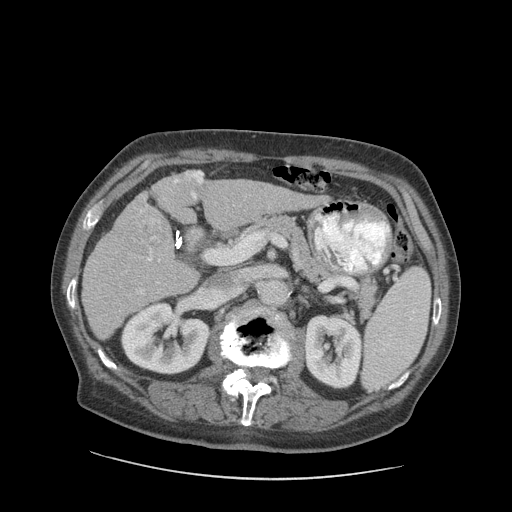
Contrast-enhanced abdominal CT (liver protocol), one axial slice. Position 44 of 89 along the scan axis. Reconstruction kernel STANDARD. 140 kVp. Soft-tissue window (W 400 / L 40 HU). 512 × 512 image matrix. From the clinical record (not read from this slice): diagnosis: hepatocellular carcinoma (patient treated with transarterial chemoembolisation; whether this scan precedes or follows treatment is not stated here); TNM stage (as recorded): Stage-I.
Structures marked on this image (semi-automatic segmentation, software-assisted and operator-edited):
- liver parenchyma outside the tumour (the mass and vessels are separate outlines, so this box may not span the whole liver): bounding box (x1, y1, x2, y2) in pixels: (82, 170, 320, 340)
- mass: (119, 206, 170, 258)
- liver vessels: (94, 172, 270, 294)